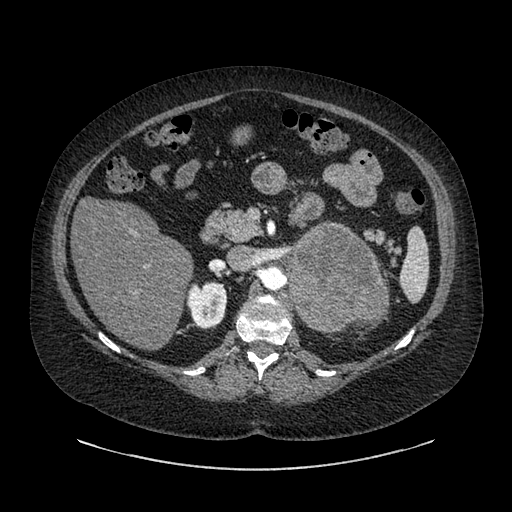
Contrast-enhanced abdominal CT, one axial slice. Position 545 of 769 along the scan axis. 120 kVp. Intravenous contrast given. Soft-tissue window (W 400 / L 40 HU). 0.62 mm slice thickness. 512 × 512 image matrix, field of view 460 × 460 mm. Female patient, age 61 years. From the clinical record (not read from this slice): diagnosis: adrenocortical carcinoma; tumour side: left adrenal; tumour size at pathology: 13 cm; Ki-67 index: 79 %.
Structures marked on this image (semi-automatic segmentation, software-assisted and operator-edited):
- mass: bounding box [x1, y1, x2, y2] px = [291, 225, 384, 331]